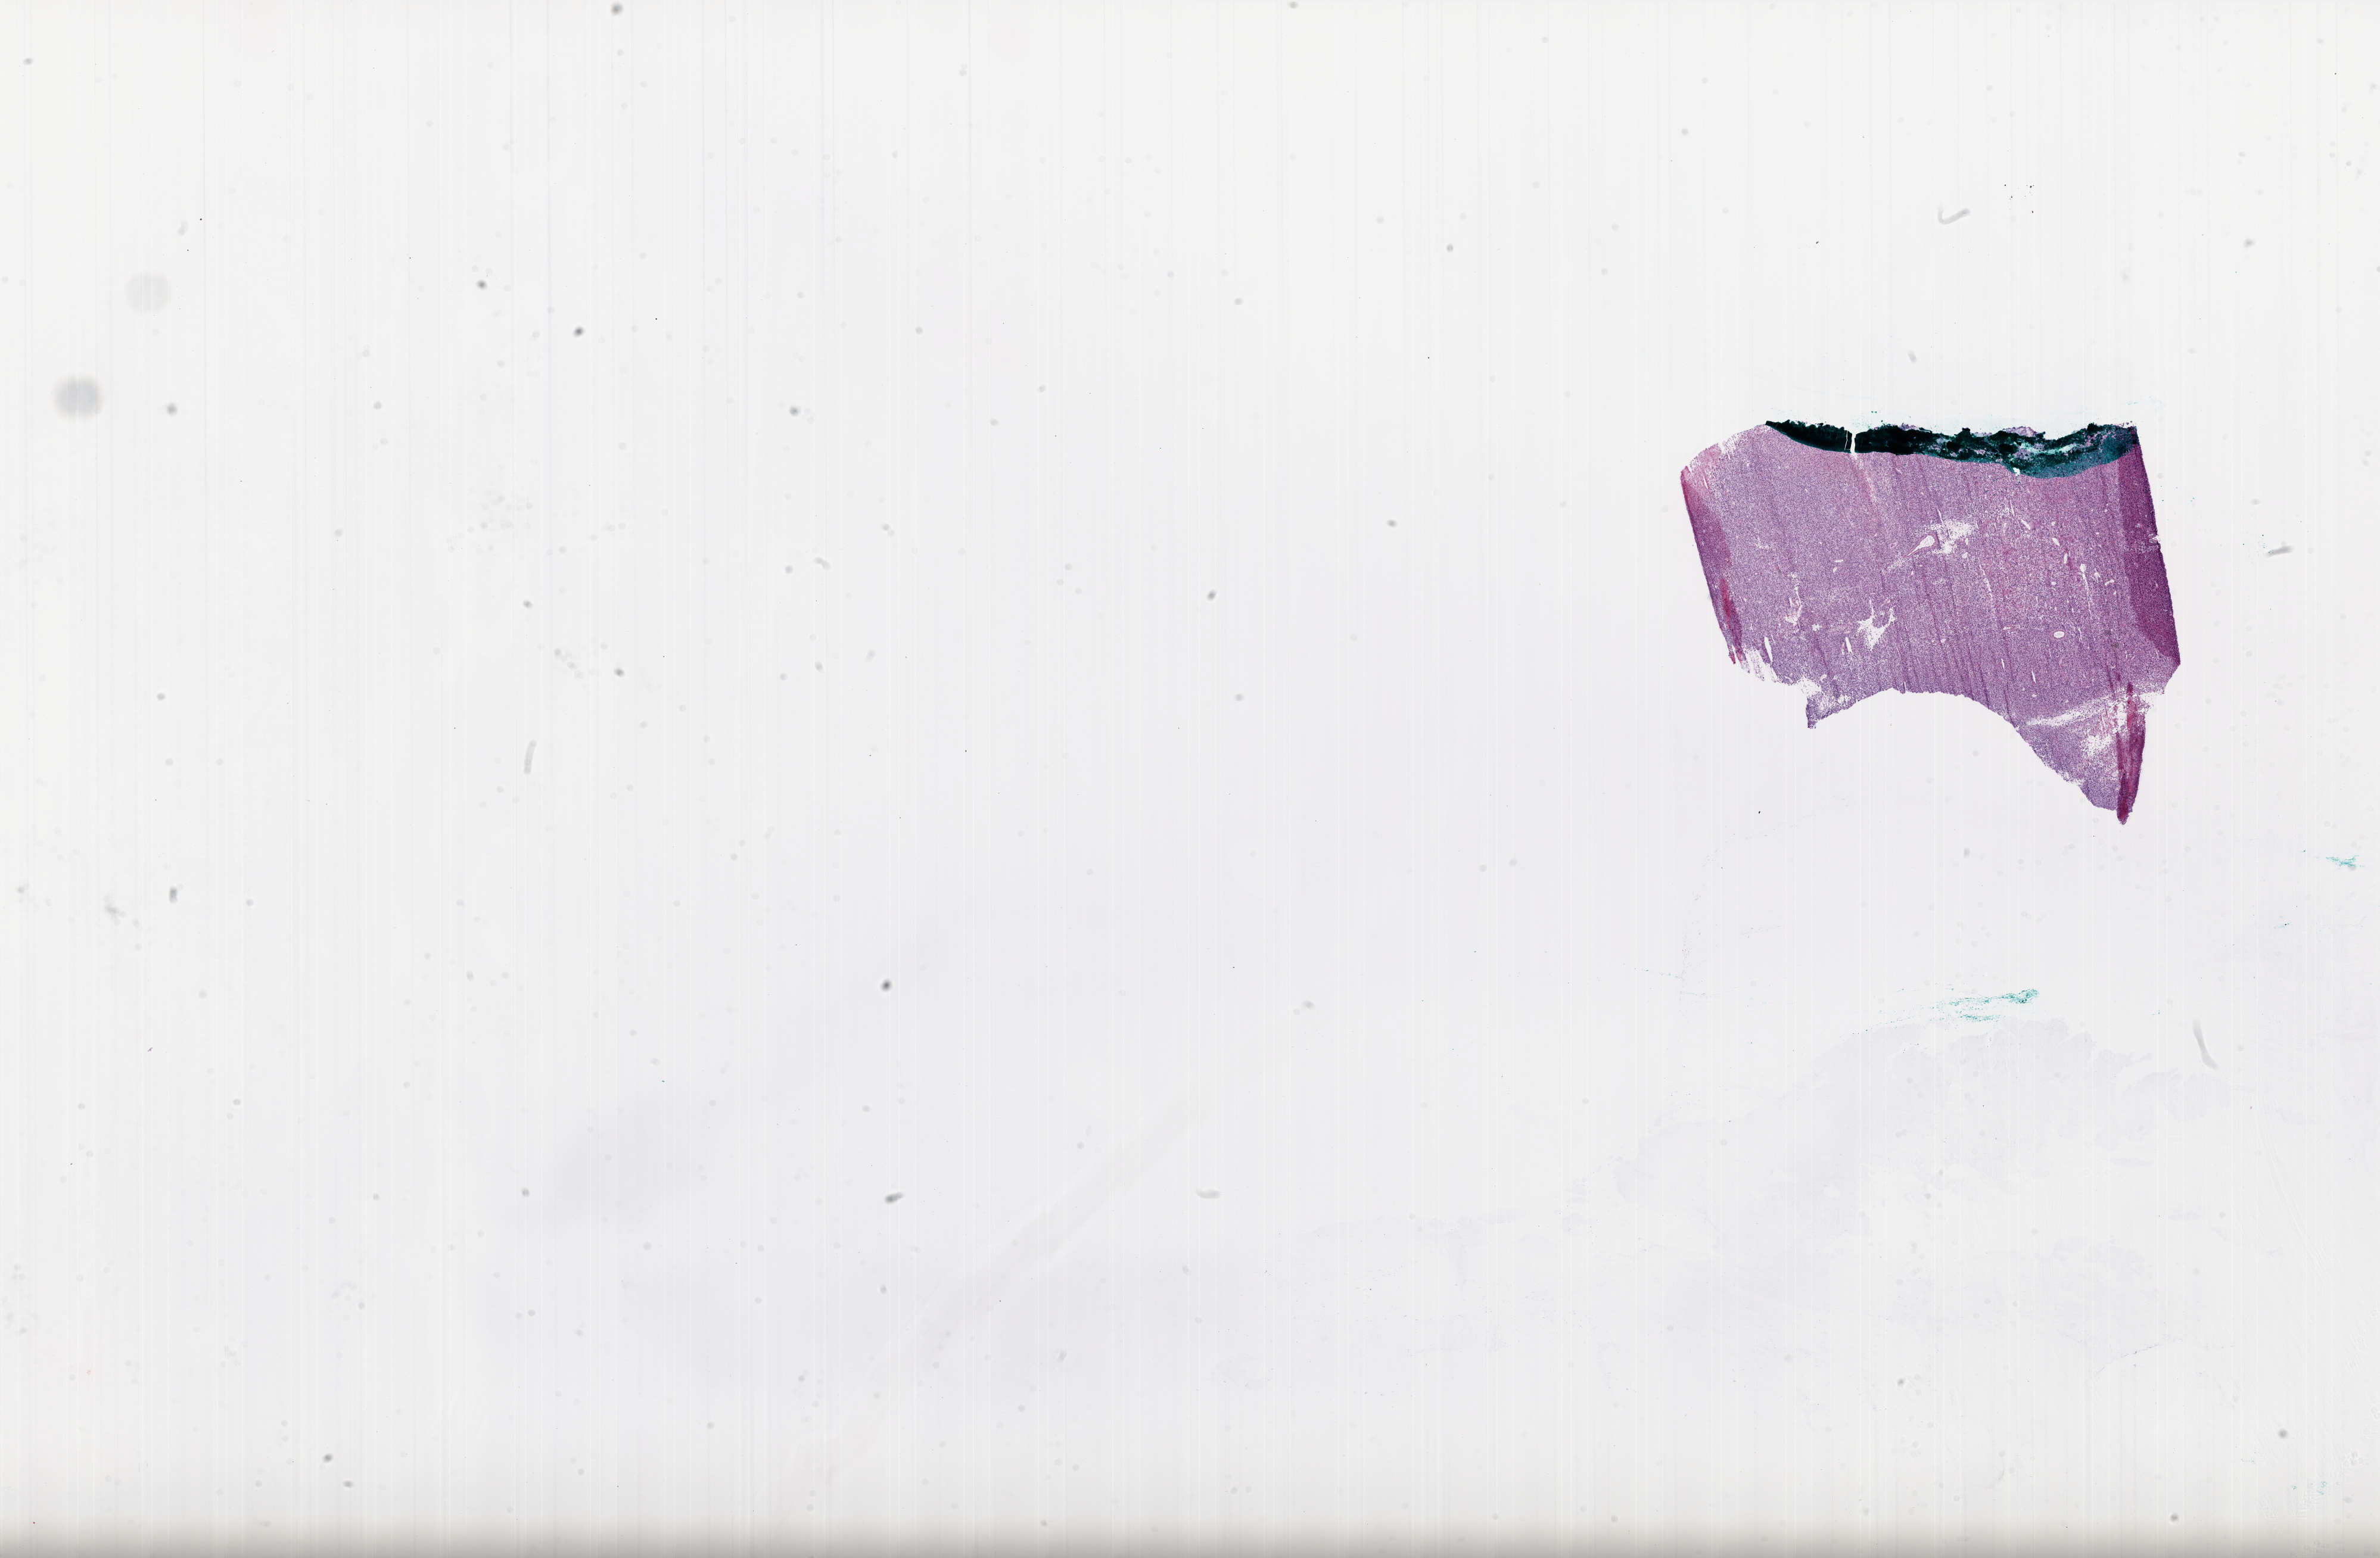
Digitized Hematoxylin and eosin (H&E) stained tissue section (whole slide), low-resolution overview of the scanned area, about 32.0 x 20.9 mm, frozen section, sample: primary tumour, brain. Male, age 71 years at initial diagnosis. Slide review estimates, as recorded: tumour cells 90%, tumour nuclei 95%, normal cells 0%, stromal cells 5%, necrosis 5%.
Histologic diagnosis: Glioblastoma.